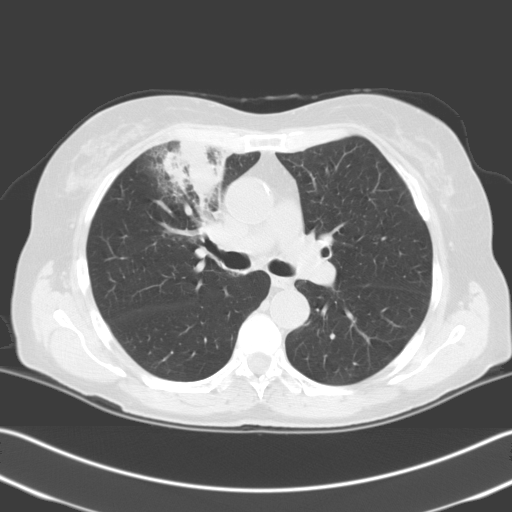
Low-dose screening chest CT, one axial slice; slice 135 of 204 in the series (ordered by position); lung window (W 1500 / L -600 HU); 512 × 512 image matrix, field of view 348 × 348 mm.
Annotated regions visible in this slice (expert manual segmentation):
- lesion 1 (tumor, upper lobe of right lung): bounding box <161,141,230,205> (left, top, right, bottom; pixels)